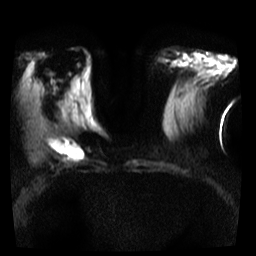
Breast MRI, one axial slice; slice 12 of 35 in the series (ordered by position); diffusion-weighted series; image 2 of 4 stored at this slice position (different b-values; order by instance number); 3 T; 256 × 256 image matrix, field of view 300 × 300 mm. Female patient.
Annotated regions visible in this slice (expert manual segmentation):
- tumour on diffusion-weighted imaging: bounding box (x1, y1, x2, y2) in pixels: (47, 135, 85, 159)